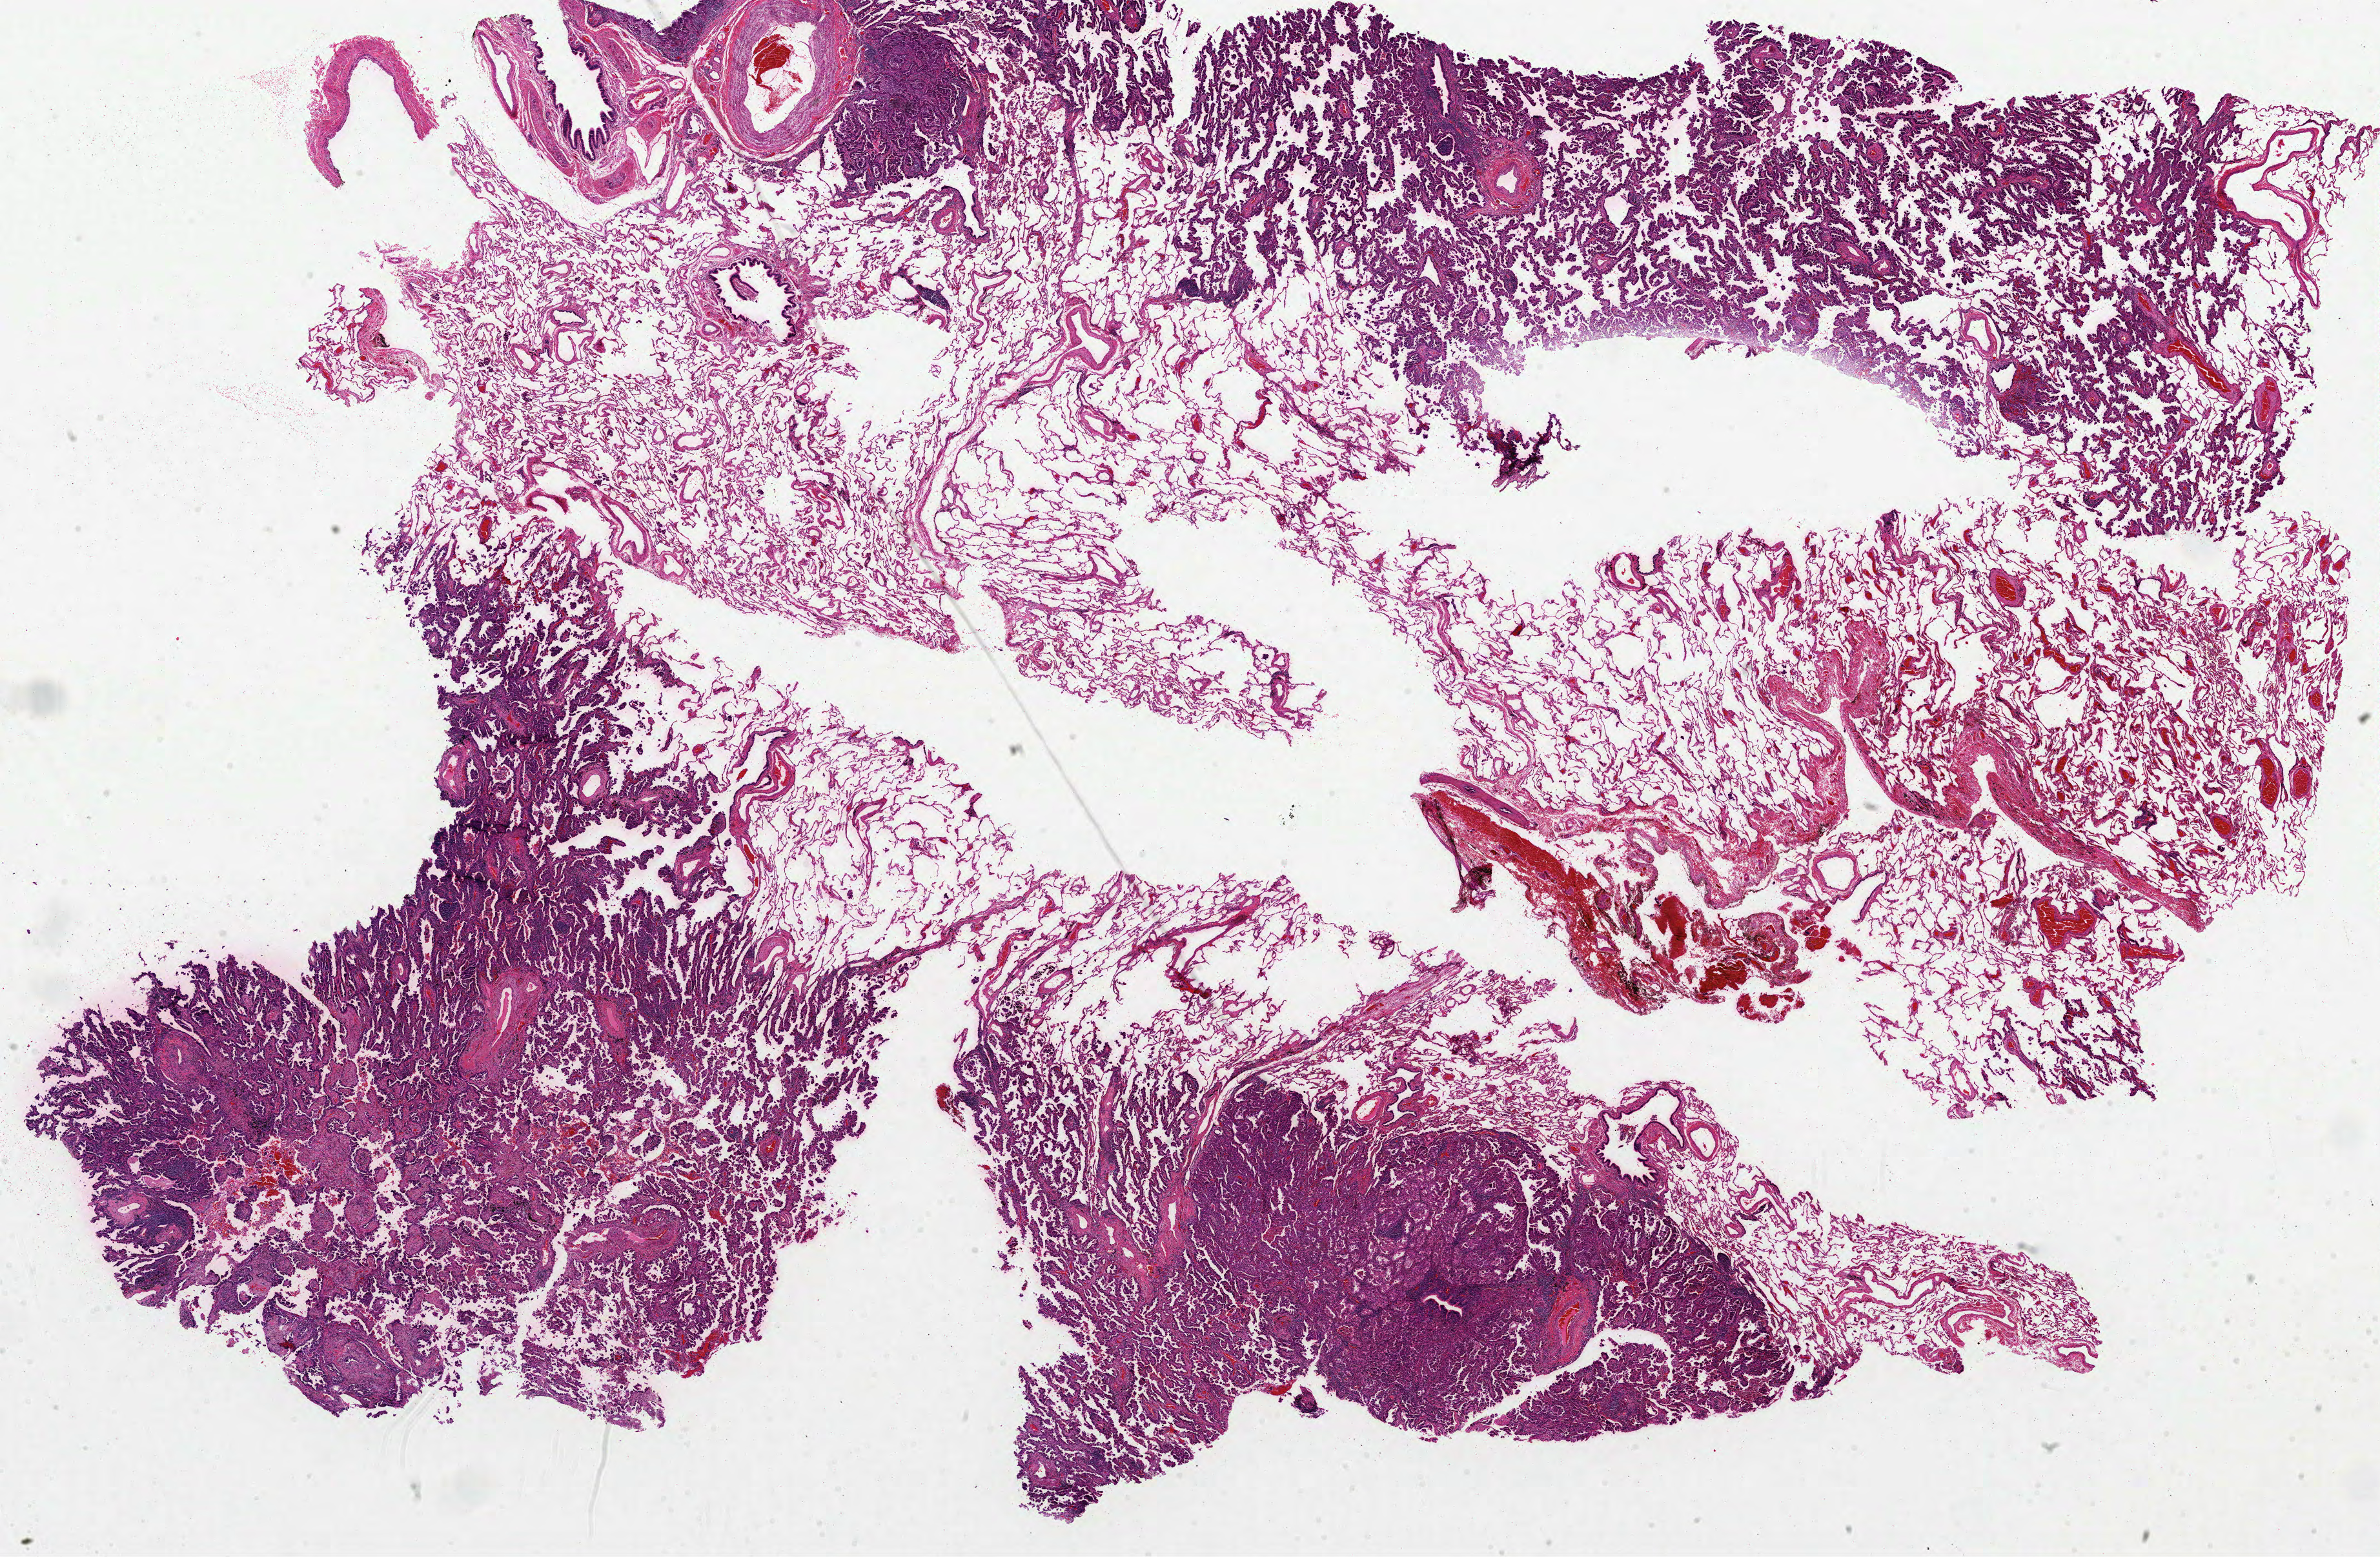
H&E-stained whole-slide image, low-resolution overview of the scanned area, about 29.7 x 19.5 mm (from a 40x scan). FFPE section. Sample: primary tumour, lung. Female, age 74 years at initial diagnosis.
AJCC pathologic stage: IA (3rd edition). Laterality: left. Diagnosis: Adenocarcinoma, NOS (lower lobe, lung).